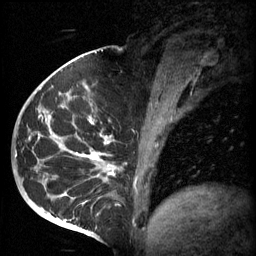
Breast MRI (dynamic contrast-enhanced), one sagittal slice; position 28 of 60 along the scan axis; 3 images stored at this slice position (order not interpretable as contrast timing); 1.5 T; TE 4.2 ms, TR 11 ms; 2 mm slice thickness; 256 × 256 image matrix. Patient: female, 51 years.
Annotated regions visible in this slice (semi-automatic segmentation, software-assisted and operator-edited):
- analysis volume of interest (the breast-tissue region the enhancement analysis was run in; not a lesion): bounding box (x1, y1, x2, y2) in pixels: (48, 82, 161, 197)
- tumour enhancement mask (voxels above the 70 % enhancement threshold inside the analysis volume of interest): (48, 86, 116, 197)